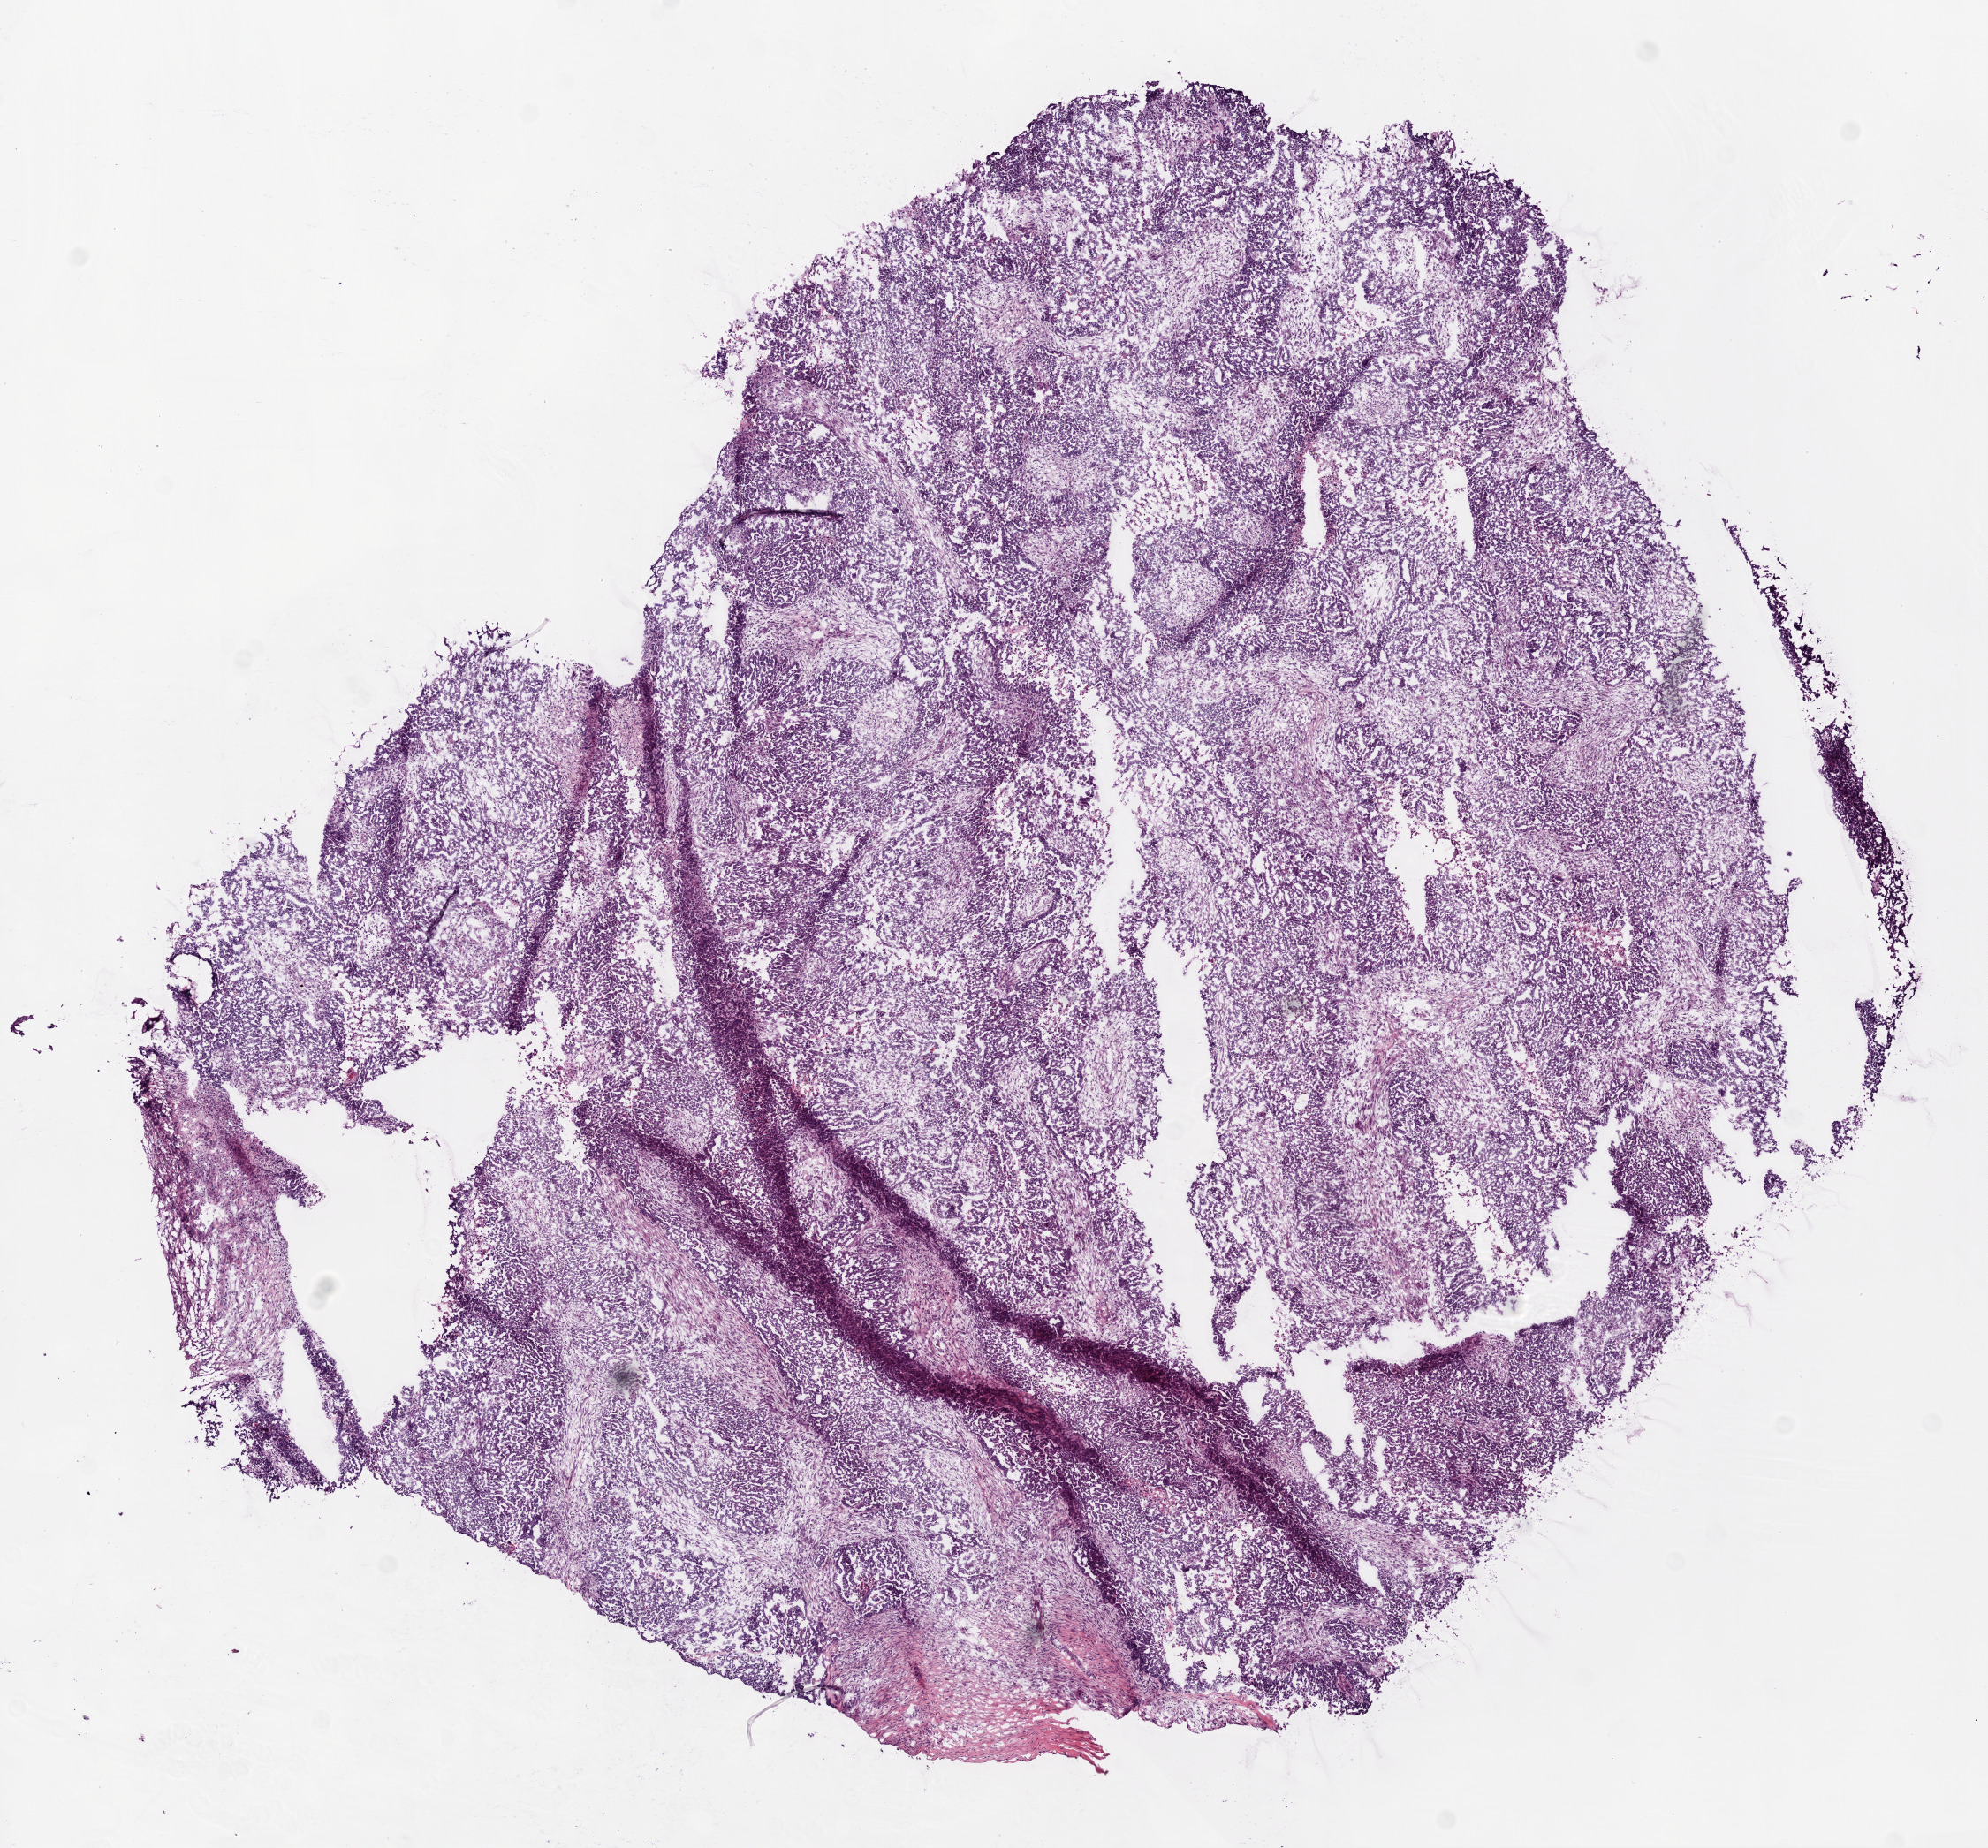
Digitized Hematoxylin and eosin (H&E) stained tissue section (whole slide), a low-resolution overview of the entire scanned area, about 9.0 x 8.4 mm. Frozen section from the bottom of the tissue portion. Primary tumour sample from the ovary. Female, age 66 years at initial diagnosis. Histologic grade: G3 (poorly differentiated). Composition of this section per pathologist review: tumour cells 89%, tumour nuclei 90%, normal cells 0%, stromal cells 10%, necrosis 1%.
FIGO stage: IIIC. Histologic diagnosis: Serous cystadenocarcinoma, NOS.